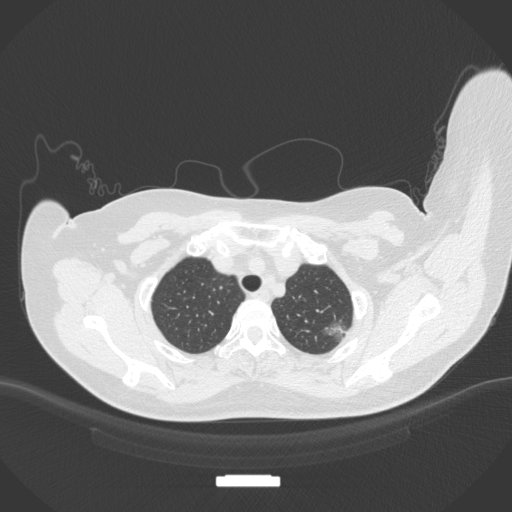
Chest CT, one axial slice; slice 316 of 386 in the series (ordered by position); lung window (W 1500 / L -600 HU); 1 mm slice thickness; 512 × 512 image matrix. Patient: female, 58 years. Case-level facts recorded for this patient, not image findings: clinical TNM (as recorded): T1c N0 M0.
Annotated regions visible in this slice (bounding box drawn by a radiologist):
- lung tumour (recorded histology: adenocarcinoma): bounding box [x1, y1, x2, y2] px = [323, 320, 353, 341]